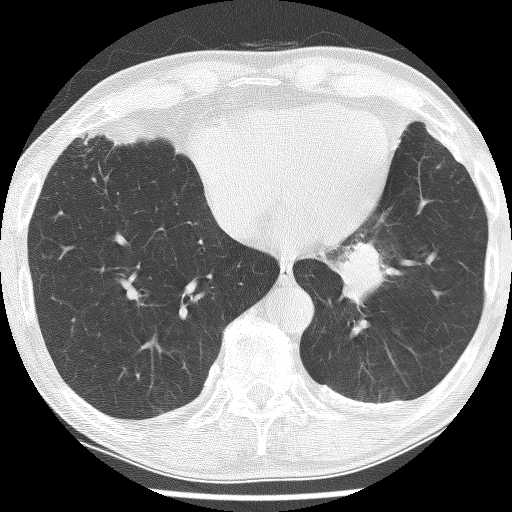
Chest CT (low-dose screening protocol), one axial image. First (baseline) screen. Lung window (W 1500 / L -600 HU). Lung (sharp) reconstruction kernel (BONE). 512 × 512 image matrix. Male participant, aged 74 years at enrolment. Current smoker at enrolment.
• Expert-annotated lung lesion, bounding box <316,225,421,318> (left, top, right, bottom; pixels).
• Screening reader's record for this exam (one nodule recorded; not confirmed to be the boxed lesion): non-calcified nodule or mass ≥4 mm, left lower lobe, 30 × 27 mm, spiculated (stellate) margins, soft tissue attenuation.
• Official screen result: positive, change unspecified: nodule(s) >= 4 mm or enlarging nodule(s), mass(es), or other non-specific abnormalities suspicious for lung cancer.
• Participant outcome: lung cancer diagnosed 151 days after this screen — adenocarcinoma, NOS, left lower lobe, stage IIIA (AJCC 6th edition), 49 mm at pathology.